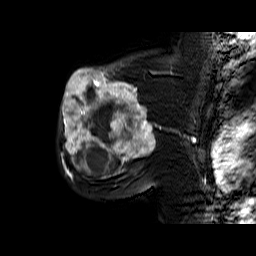
Breast MRI (dynamic contrast-enhanced), one sagittal slice; slice 42 of 60 in the series (ordered by position); dynamic contrast-enhanced series, time point 2 of 6 at this slice position (early post-contrast); 1.5 T; TE 6.4 ms, TR 32.9 ms; 4 mm slice thickness; 256 × 256 image matrix, field of view 200 × 200 mm. Female patient. Case-level facts recorded for this patient, not image findings: setting: breast cancer imaged before/during neoadjuvant chemotherapy; receptor status: triple-negative.
Structures marked on this image (semi-automatically segmented with operator editing):
- analysis volume of interest (the breast-tissue region the enhancement analysis was run in; not a lesion): bounding box [x1, y1, x2, y2] px = [59, 65, 159, 174]
- tumour enhancement mask (voxels above the 100 % enhancement threshold inside the analysis volume of interest): [61, 65, 156, 174]